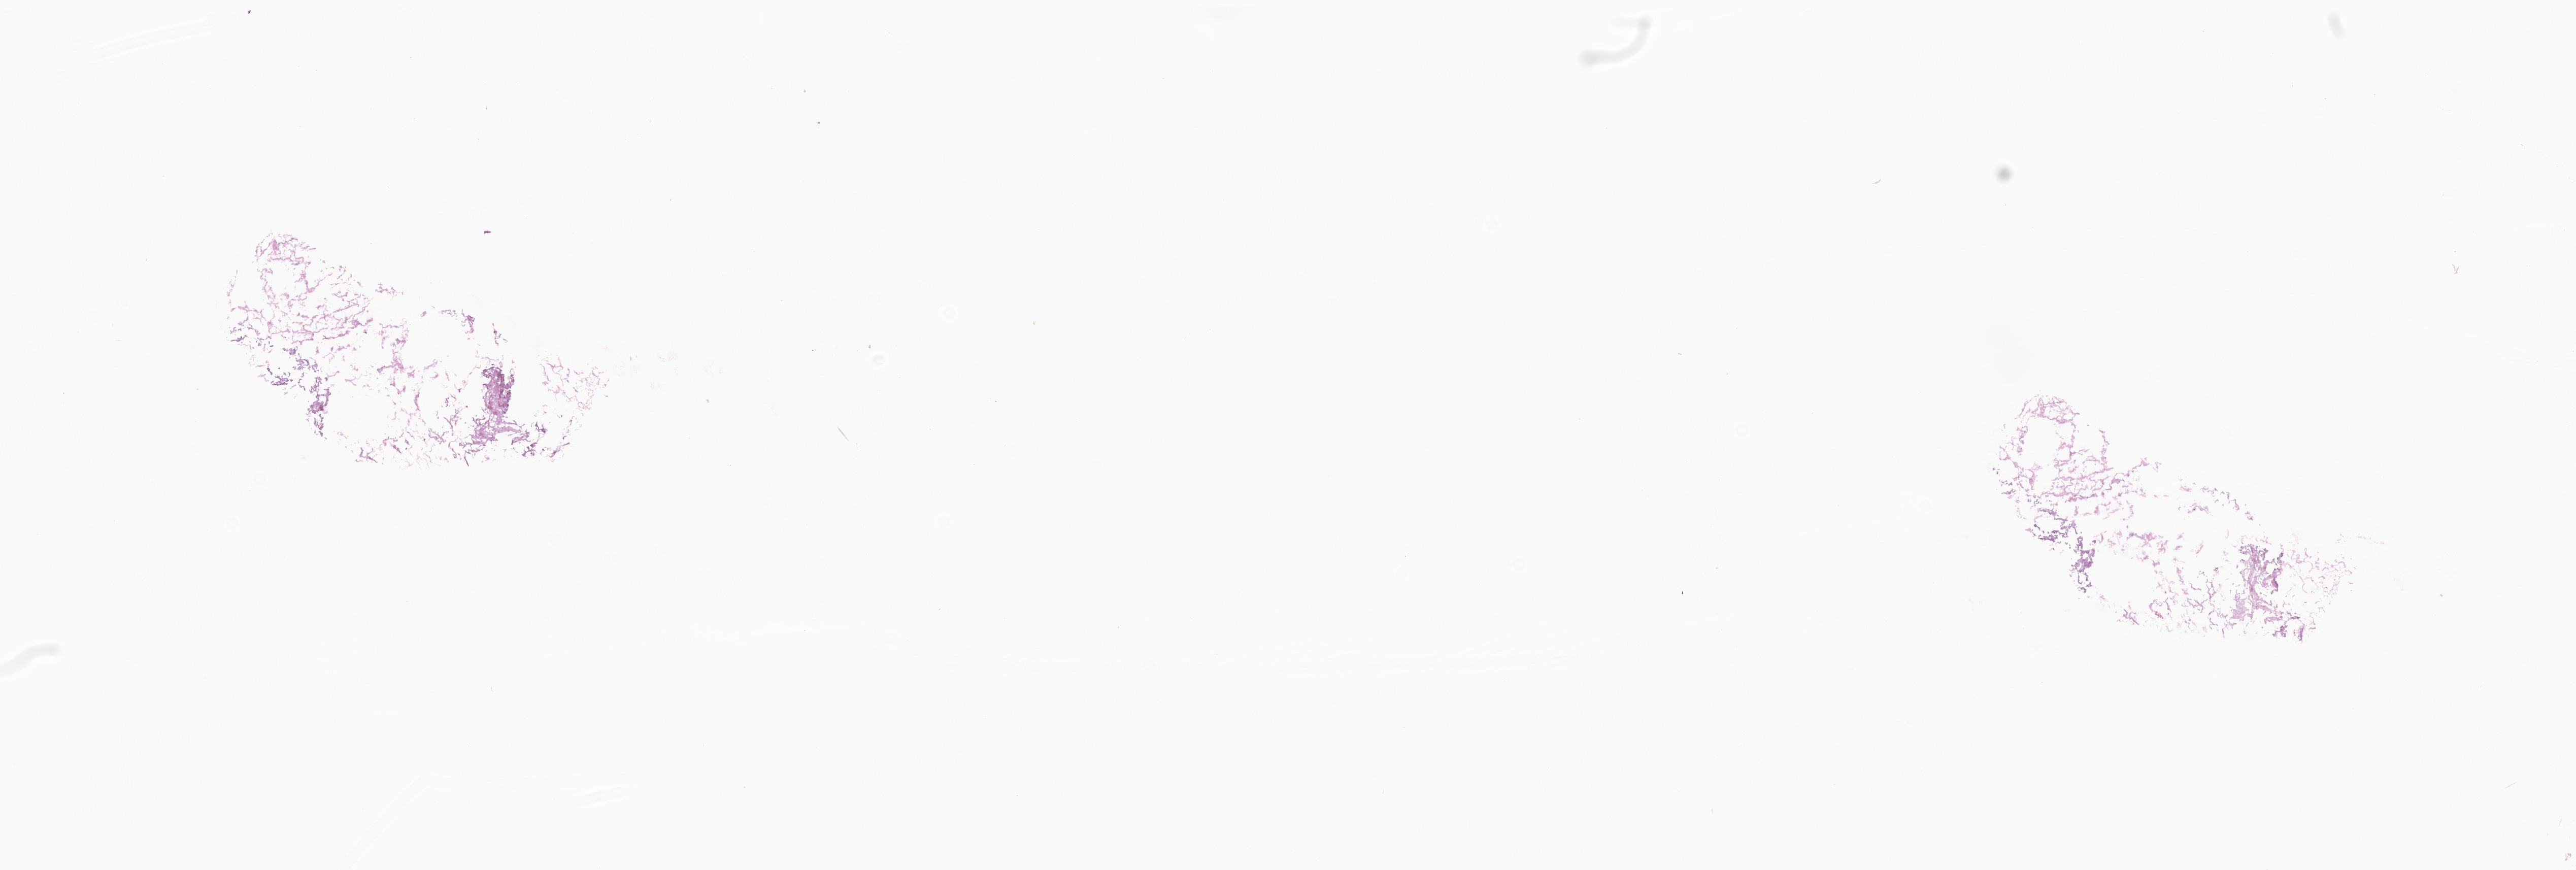
Whole-slide image, hematoxylin and eosin (H&E) stain — whole scanned area (about 21.4 x 7.2 mm) shown as a low-resolution overview. Frozen section (tissue freezing medium). Normal-tissue sample (non-tumor) from a patient with leiomyosarcoma, NOS. Female patient; age at initial diagnosis 60 years. Composition of this section per pathologist review: tumor cells 0%, tumor nuclei 0%, stromal cells 0%, necrosis 0%, normal cells 100%. Infiltration values recorded for this section: lymphocyte infiltration 0%, monocyte infiltration 0%, neutrophil infiltration 0%.
• this section: non-tumor tissue sample; the patient's diagnosis is given above
• section: top of the tissue portion